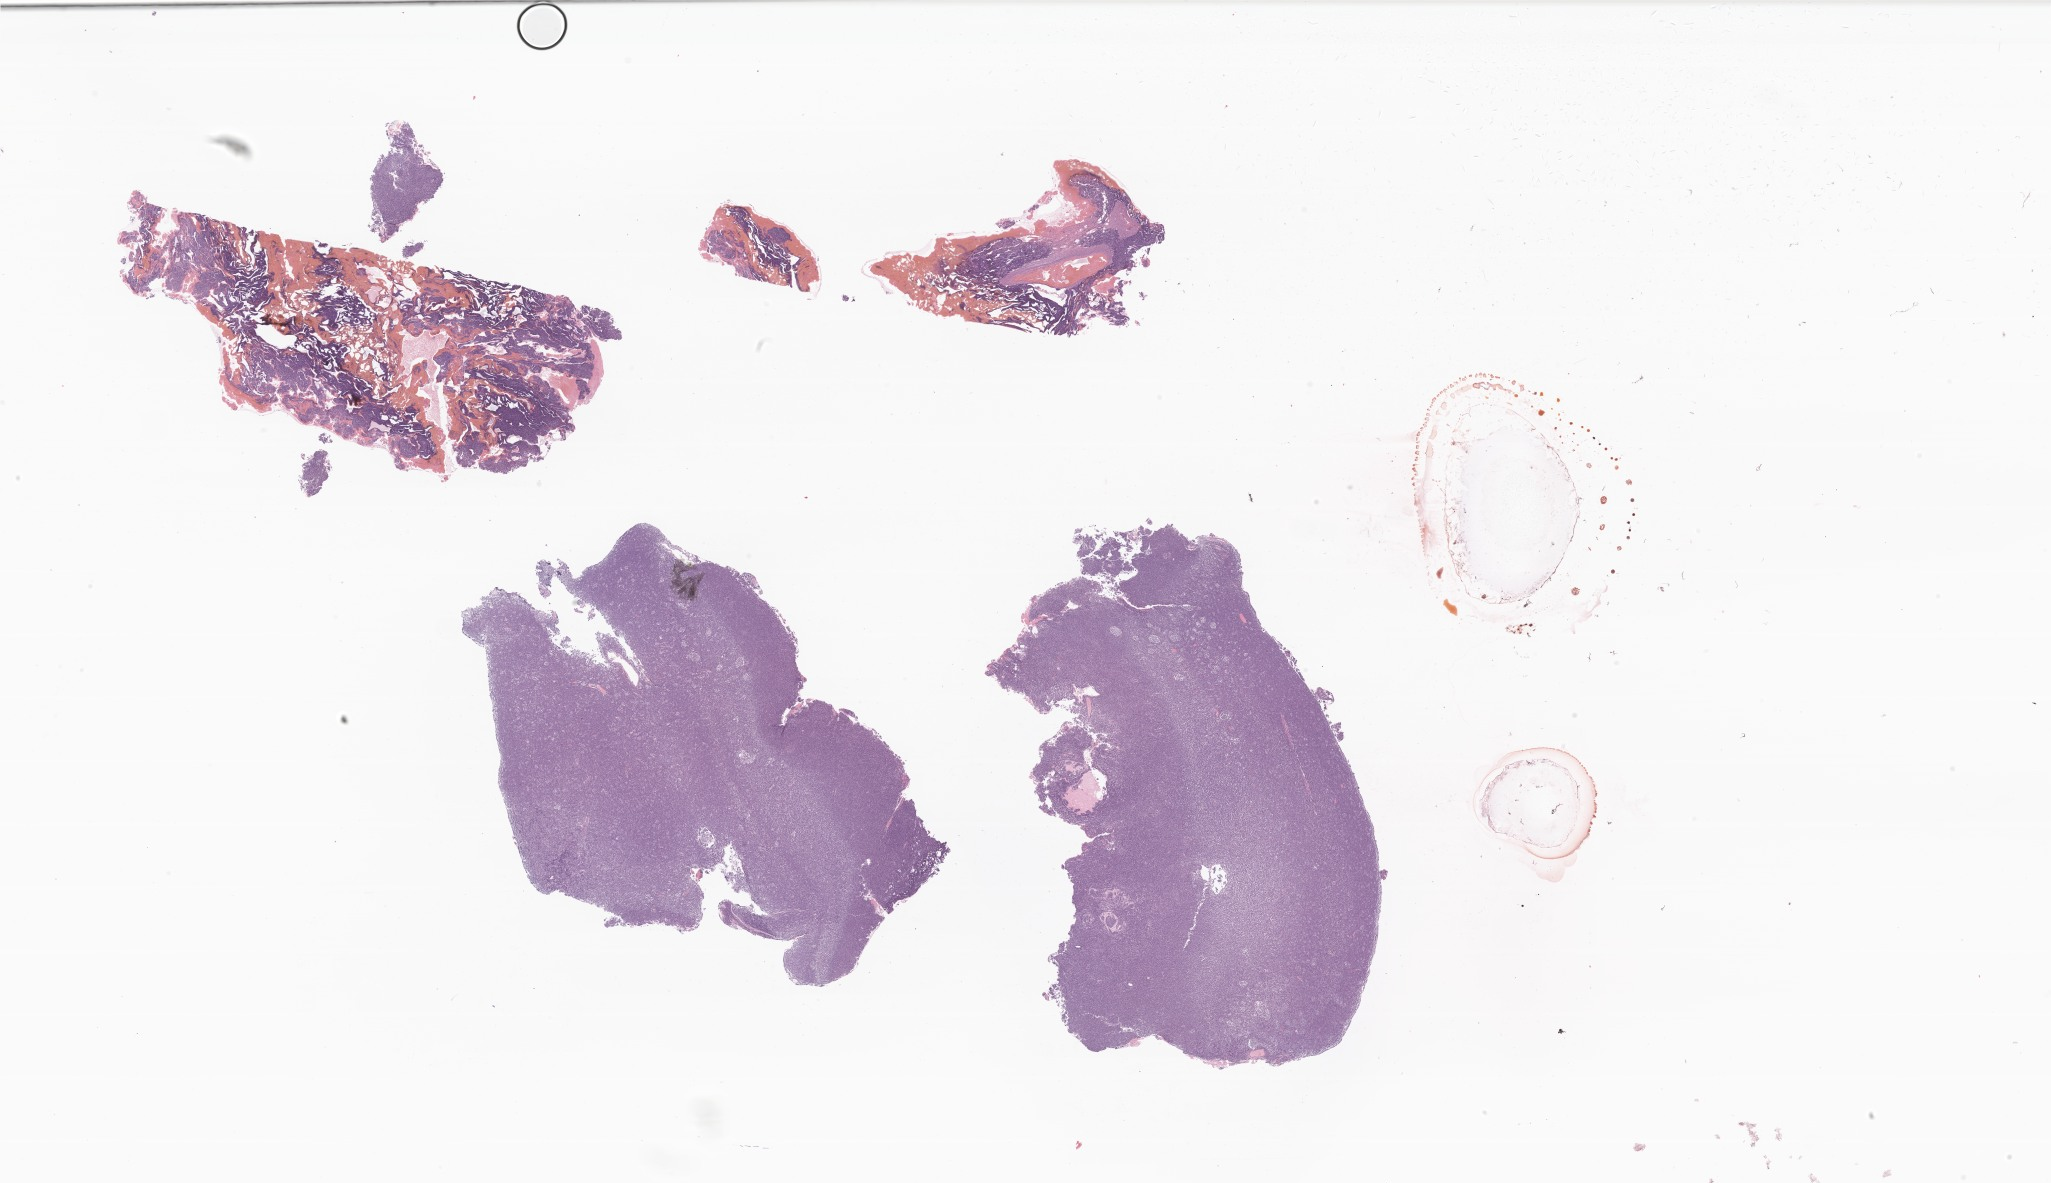
Whole-slide image, H&E stain of tumor tissue from the cerebellum, a low-resolution overview of the entire scanned area, about 34.6 x 20.0 mm. Formalin-fixed paraffin-embedded section. Male patient, age 143 months (11 years 11 months).
- recorded diagnosis: Medulloblastoma, NOS